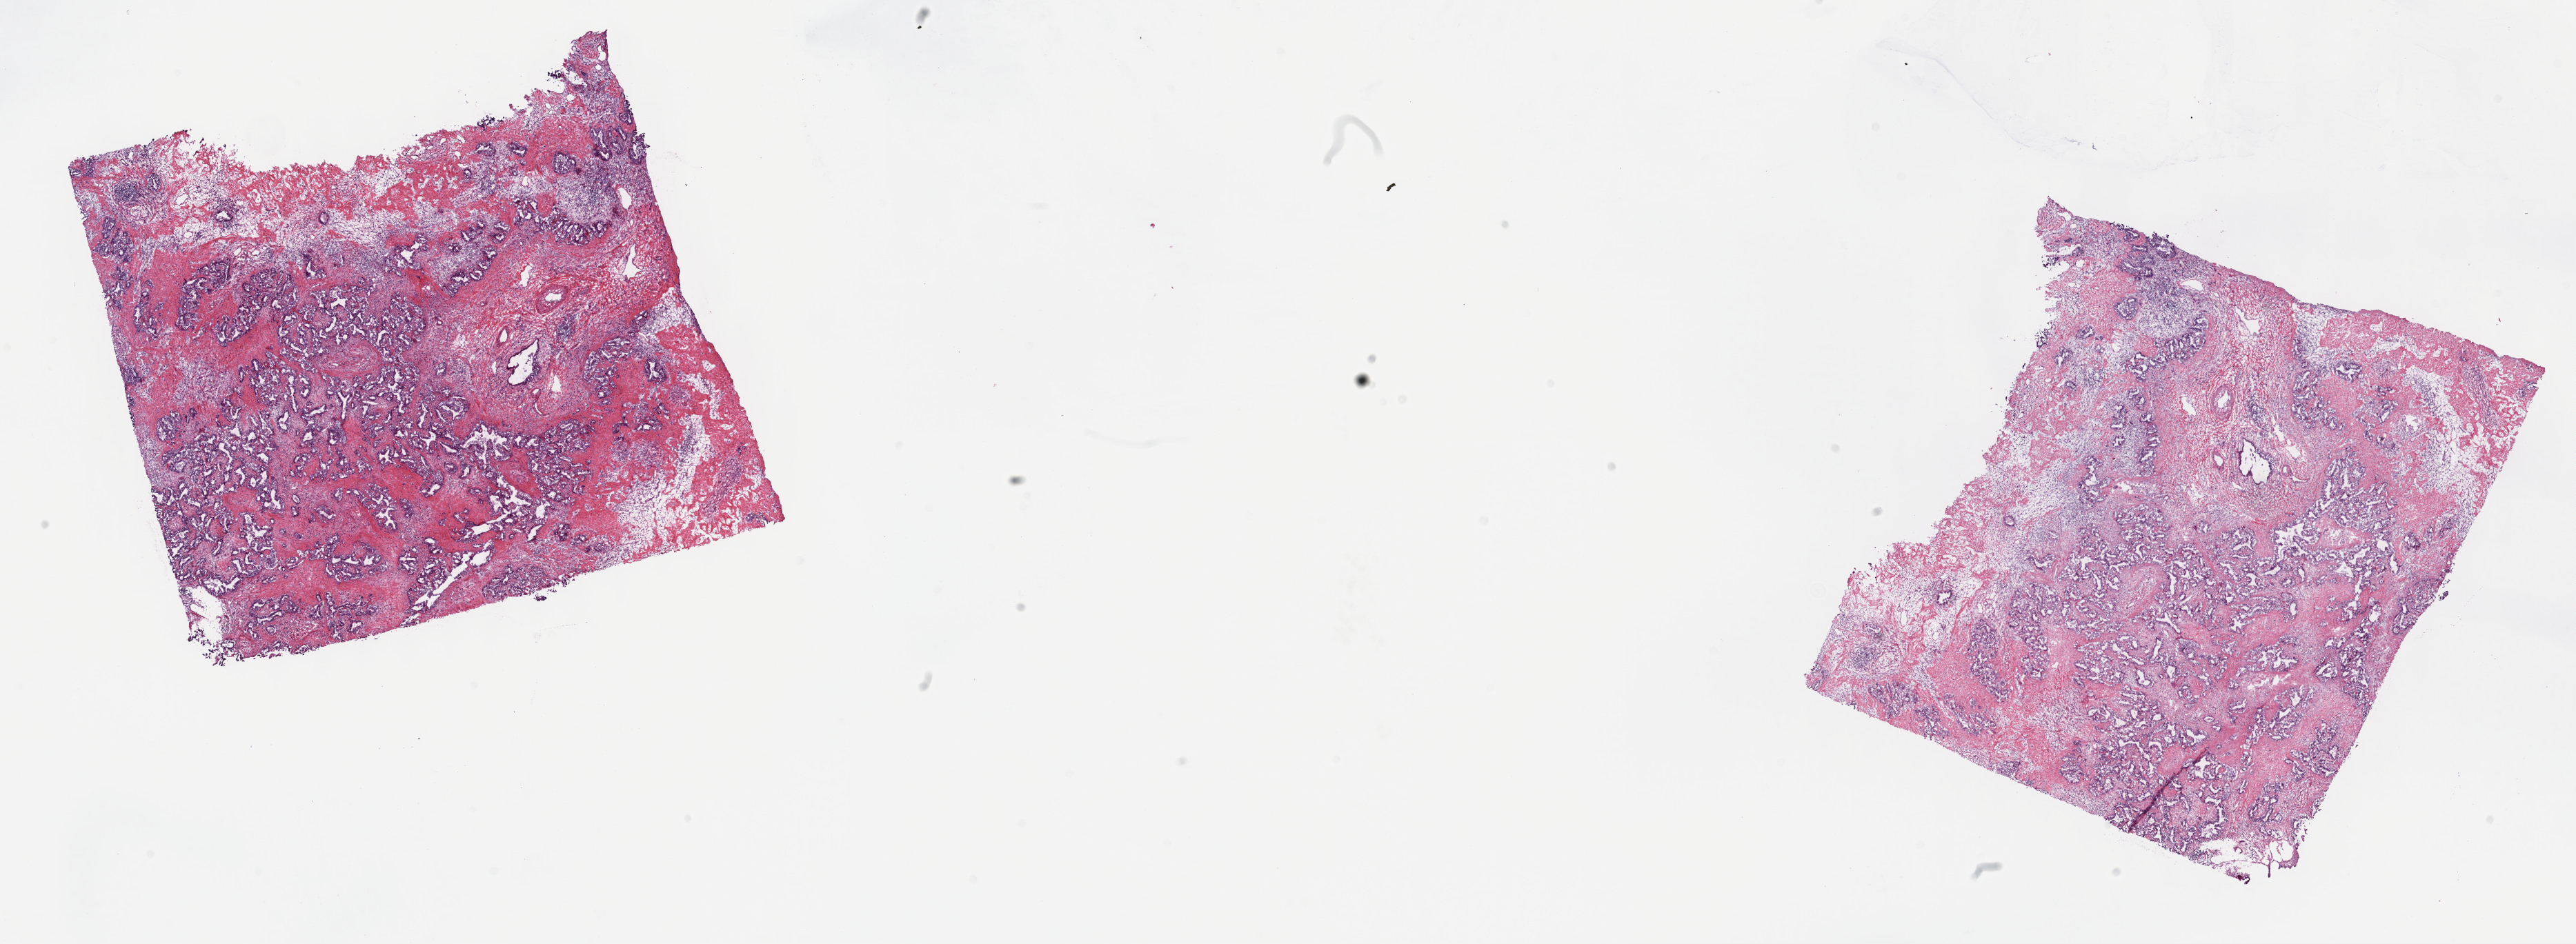
Whole-slide histology image, H&E-stained, low-resolution overview of the scanned area, about 30.2 x 11.1 mm (from a 40x scan); frozen section from the top of the tissue portion; sample: primary tumour, bile duct. Male, age 82 years at initial diagnosis. Histologic grade: G3 (poorly differentiated). Slide review estimates, as recorded: tumour cells 75%, tumour nuclei 75%, normal cells 0%, stromal cells 25%, necrosis 0%. Inflammatory infiltration, as recorded: lymphocyte infiltration 3%, monocyte infiltration 1%, neutrophil infiltration 3%.
* AJCC pathologic stage: I (7th edition)
* pathologic diagnosis: Cholangiocarcinoma